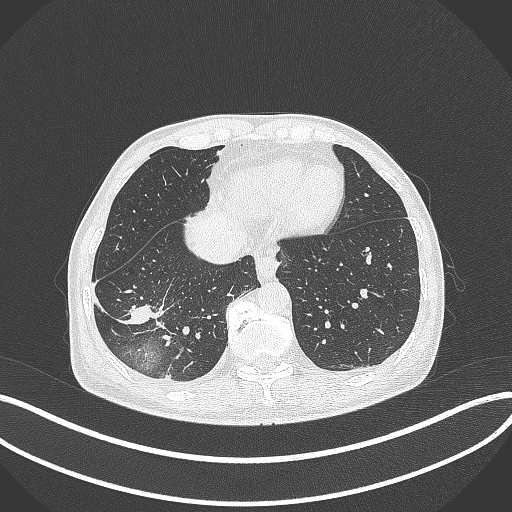
Chest CT, one axial slice; position 96 of 388 along the scan axis; 120 kVp; lung window (W 1500 / L -600 HU); 512 × 512 image matrix, field of view 400 × 400 mm. Male patient, age 64 years. Case-level facts recorded for this patient, not image findings: clinical TNM (as recorded): T3 N0 M0.
Outlined on this slice (bounding box drawn by a radiologist):
- lung tumour (recorded histology: adenocarcinoma): box from (x=115, y=301) to (x=170, y=326) px